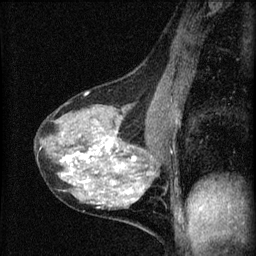
Breast MRI (dynamic contrast-enhanced), one sagittal slice. Slice 31 of 60 in the series (ordered by position). Dynamic contrast-enhanced series, image 2 of 4 at this slice position (ordered by acquisition). 1.5 T. TE 4.2 ms, TR 8.2 ms. 2 mm slice thickness. 256 × 256 image matrix. Female patient, age 41 years.
Structures marked on this image (semi-automatically segmented with operator editing):
- analysis volume of interest (the breast-tissue region the enhancement analysis was run in; not a lesion): bounding box [x1, y1, x2, y2] px = [35, 91, 166, 208]
- tumour enhancement mask (voxels above the 70 % enhancement threshold inside the analysis volume of interest): [40, 129, 126, 208]